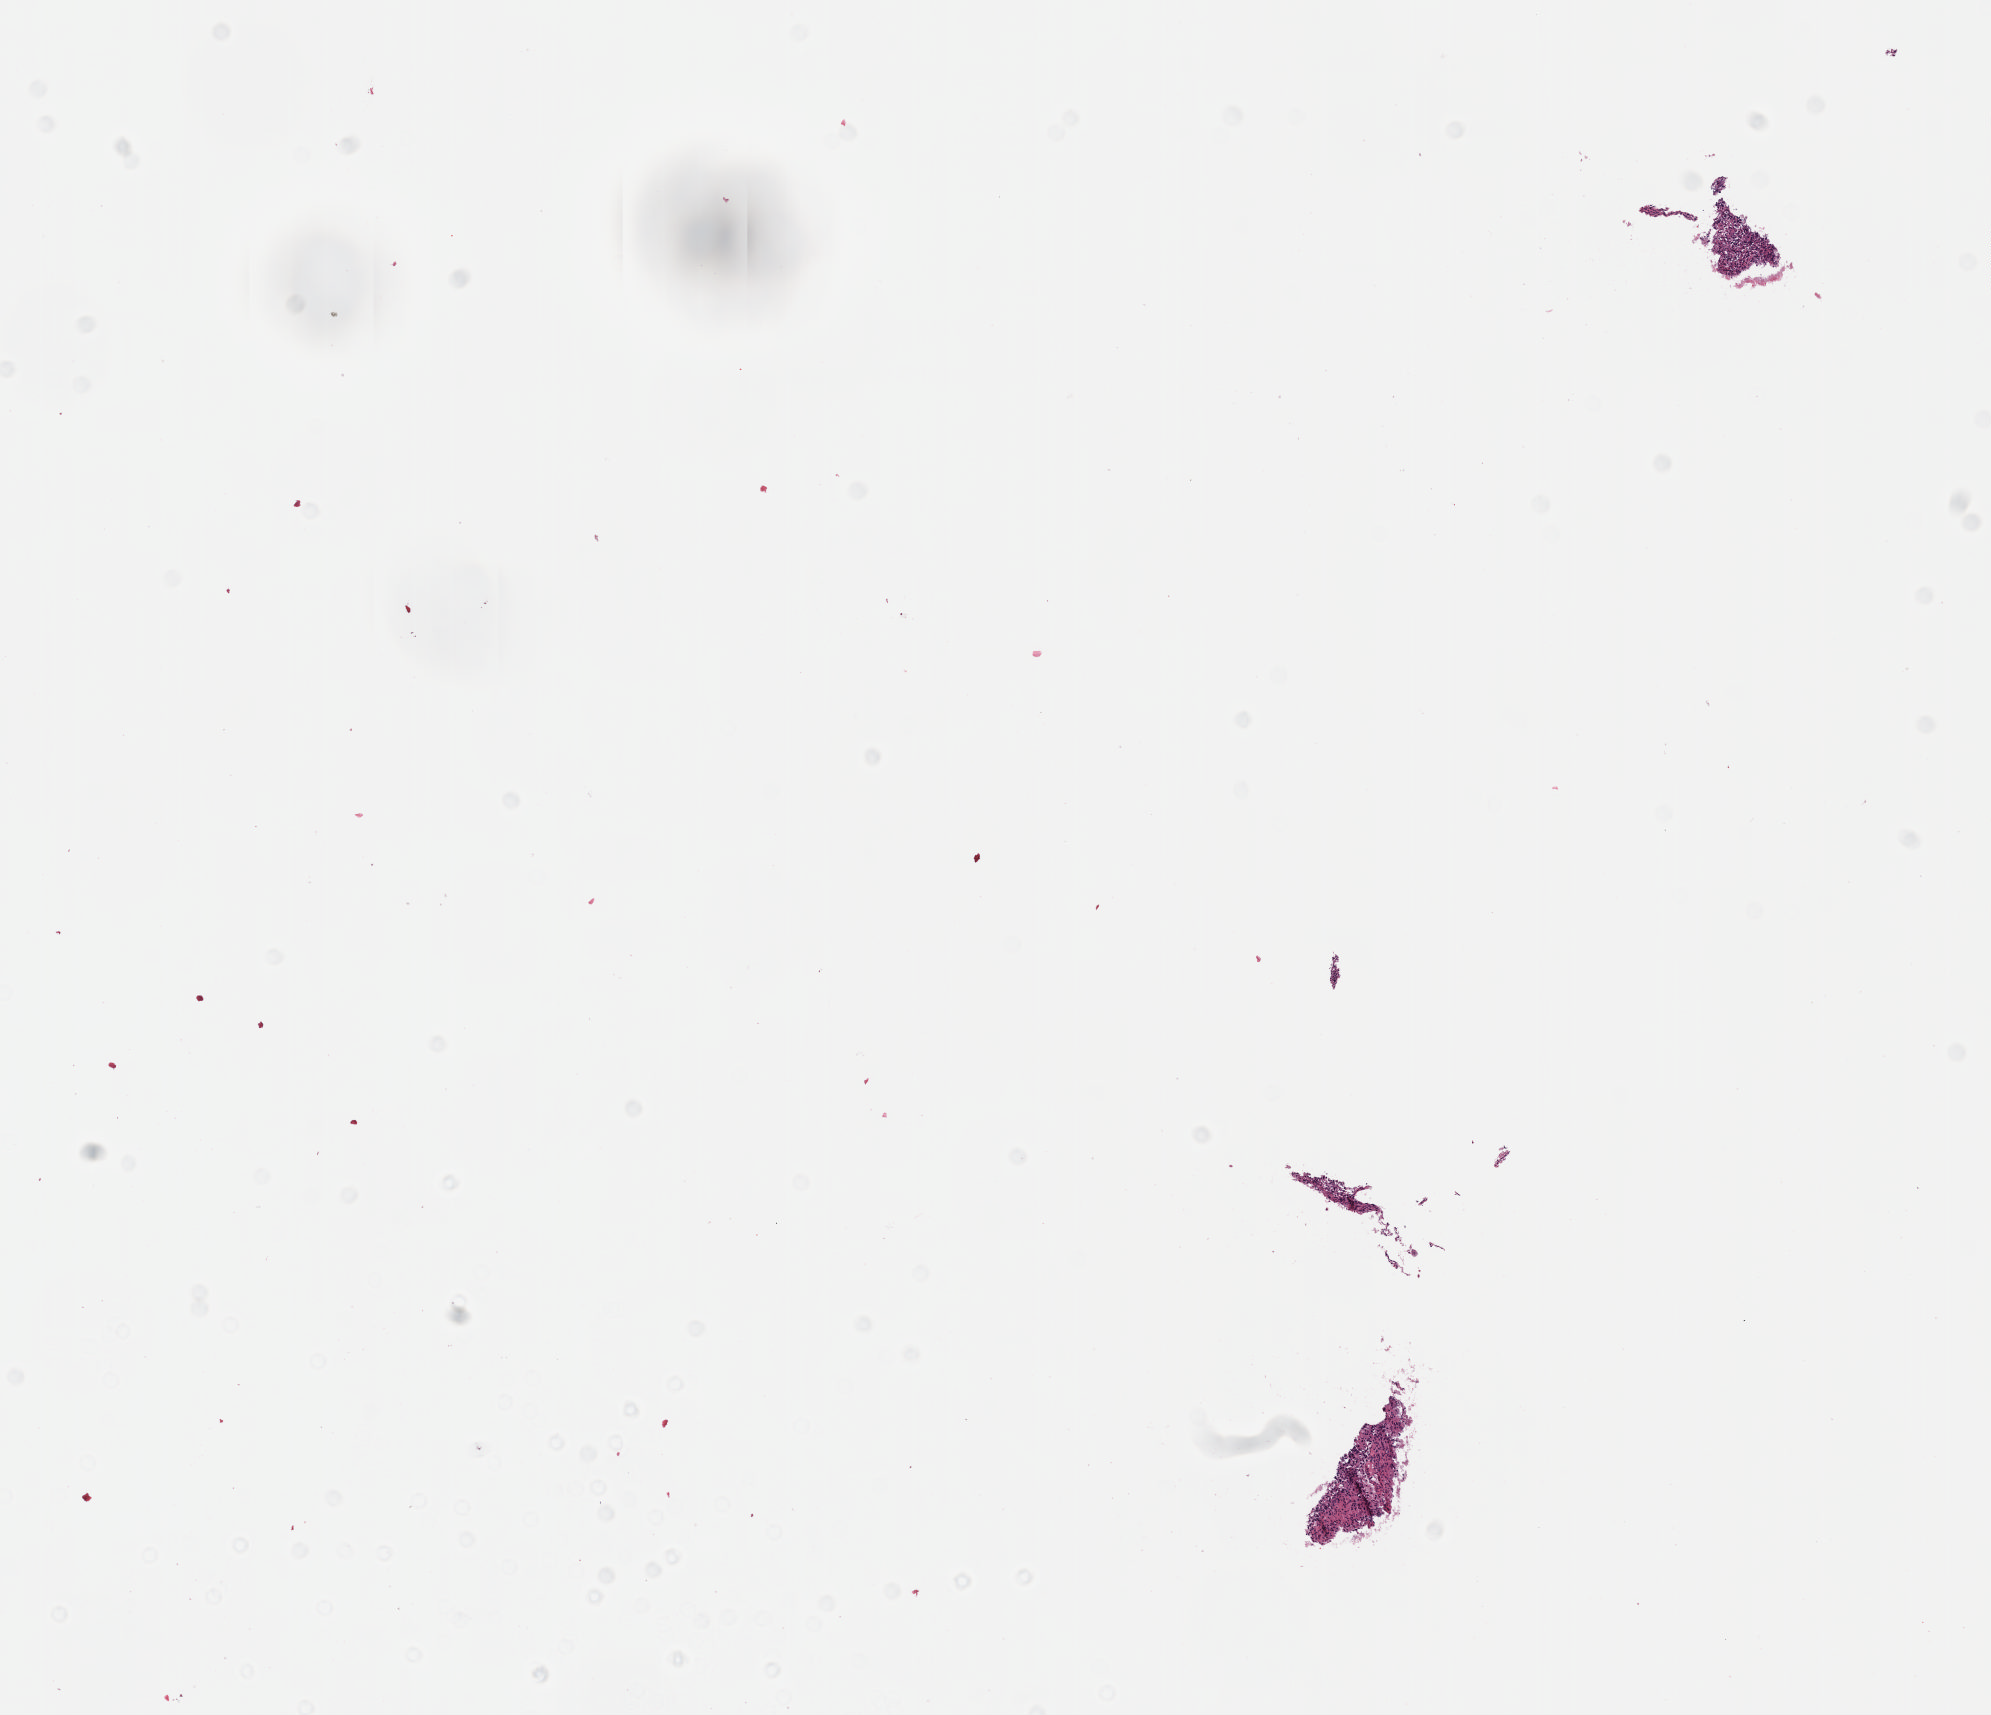
Digitized H&E-stained tissue section (whole slide), a low-resolution overview of the entire scanned area, about 8.1 x 6.9 mm. FFPE section. Primary tumour sample from the brain. Male patient; age at initial diagnosis 14 years.
Pathologic diagnosis: Mixed glioma (cerebrum).